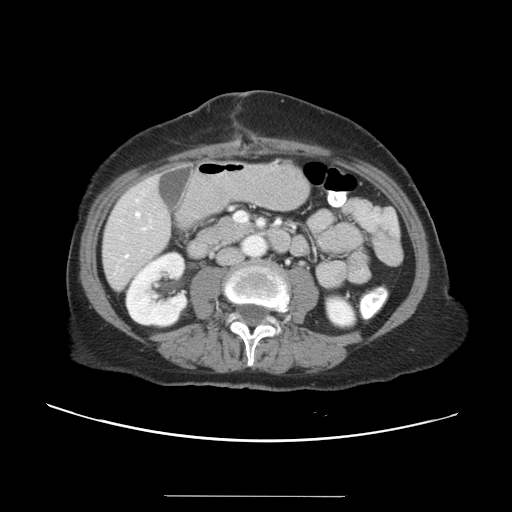
Contrast-enhanced abdominal CT, one axial slice. Intravenous contrast given. Soft-tissue window (W 400 / L 40 HU). 5 mm slice thickness. 512 × 512 image matrix. Female patient, age 69 years. Case-level facts recorded for this patient, not image findings: diagnosis: colorectal cancer liver metastases, imaged before liver resection; multiple liver metastases: yes; largest metastasis: 1.4 cm; disease in both lobes: yes.
Annotated regions visible in this slice (manually delineated by an expert):
- hepatic veins: bounding box <125,200,141,258> (left, top, right, bottom; pixels)
- liver: <104,177,171,289>
- planned liver remnant (the part of the liver to remain after resection): <104,234,166,289>
- portal vein (with intrahepatic branches): <143,212,279,230>